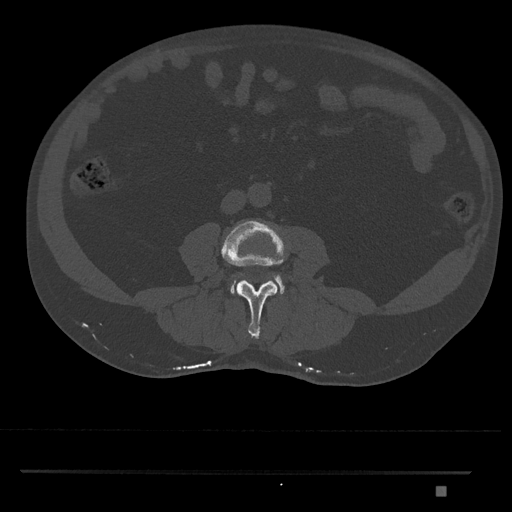
CT including the spine, one axial slice. Position 661 of 1134 along the scan axis. Reconstruction kernel Br40s/3. Bone window (W 1800 / L 400 HU). 0.5 mm slice thickness. 512 × 512 image matrix, field of view 429 × 429 mm. Male patient, age 65 years. From the clinical record (not read from this slice): primary cancer: prostate.
Structures marked on this image (semi-automatic segmentation, software-assisted and operator-edited):
- L3 vertebra: bounding box (x1, y1, x2, y2) in pixels: (221, 220, 286, 339)
- L4 vertebra: (230, 274, 285, 294)